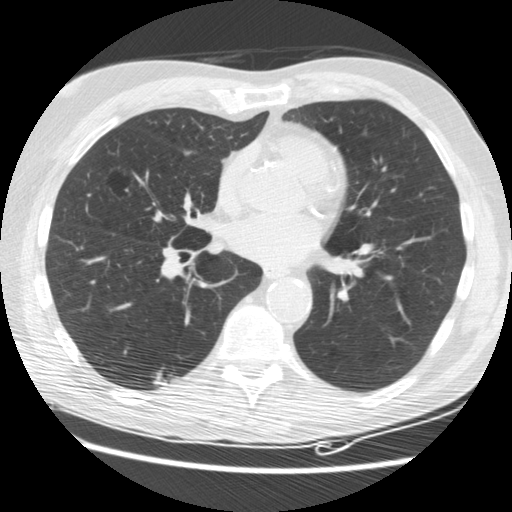
Low-dose screening chest CT, one axial slice. Position 82 of 176 along the scan axis. Reconstruction kernel STANDARD. 120 kVp. Lung window (W 1500 / L -600 HU). 2.5 mm slice thickness. 512 × 512 image matrix, field of view 347 × 347 mm.
Structures marked on this image (expert manual segmentation):
- lesion 2 (tumor, lower lobe of right lung): bounding box <152,367,174,388> (left, top, right, bottom; pixels)